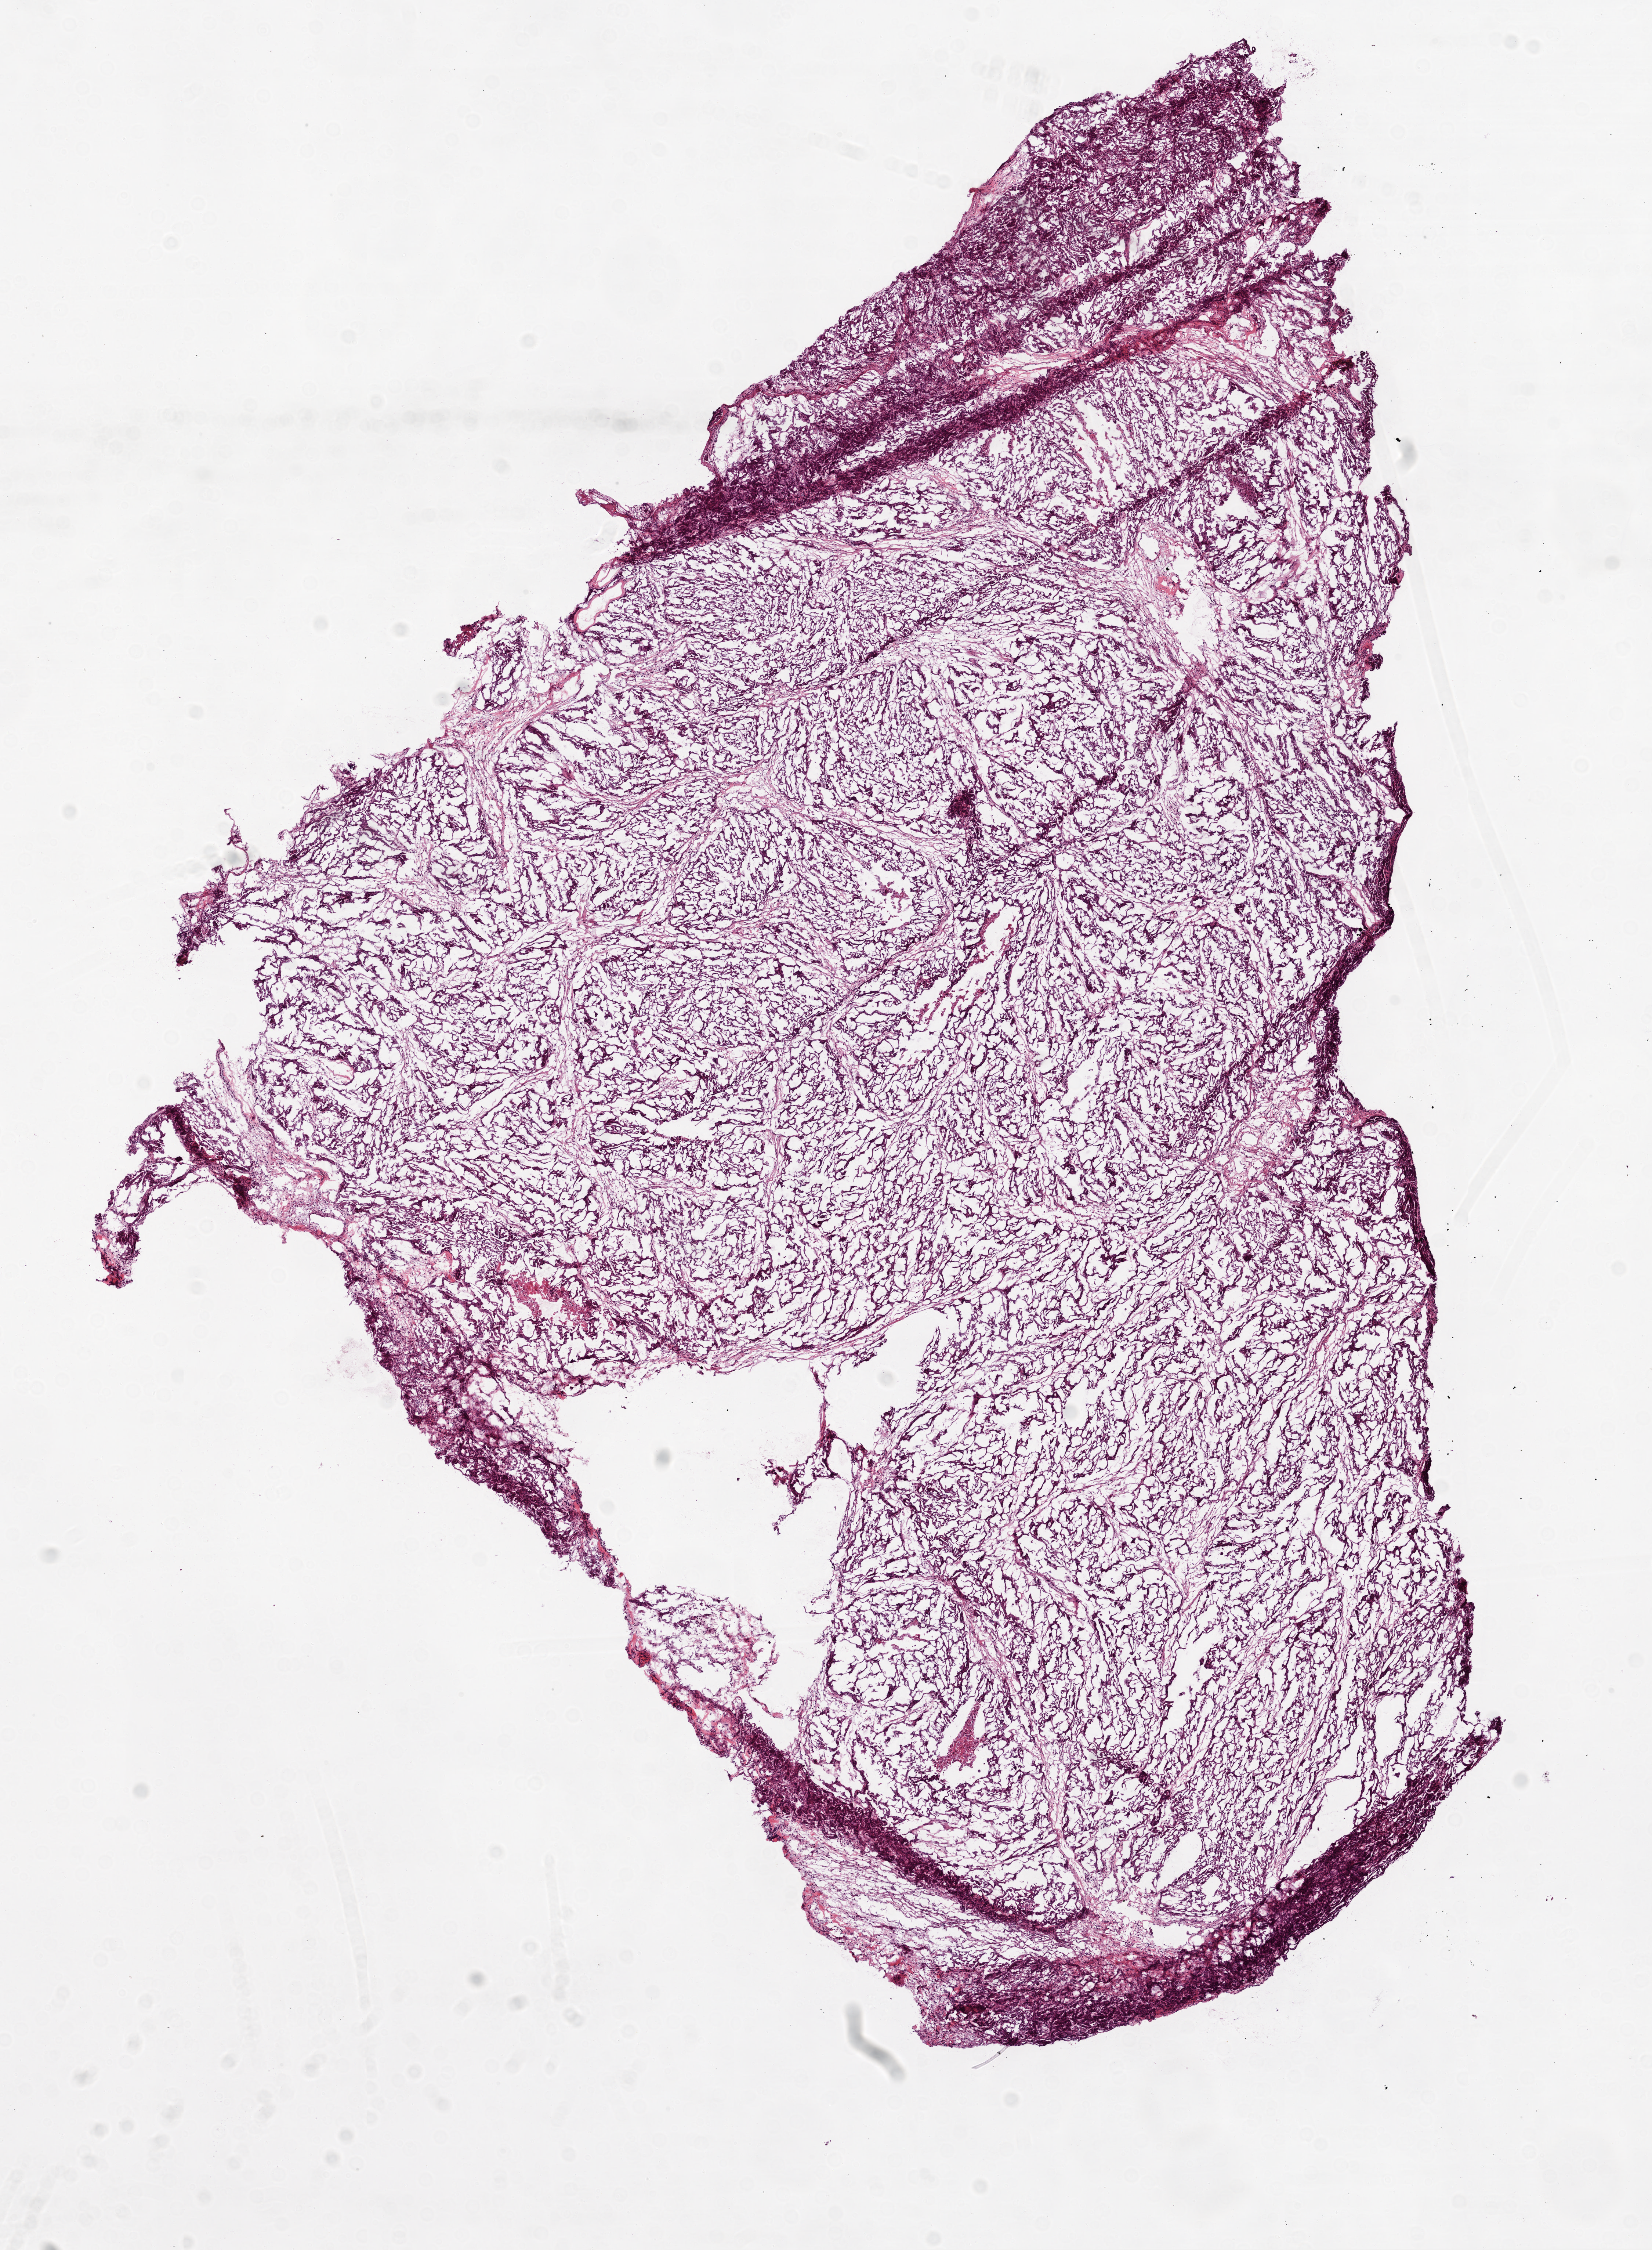
H&E-stained whole-slide image — a low-resolution overview of the entire scanned area, about 9.0 x 12.3 mm (slide scanned at 20x). Frozen section from the top of the tissue portion. Sample: primary tumour, ovary. Female patient; age at initial diagnosis 59 years. Pathologist review of this section (percent, as recorded): tumour cells 85%, tumour nuclei 90%.
Pathologic diagnosis: Serous cystadenocarcinoma, NOS.